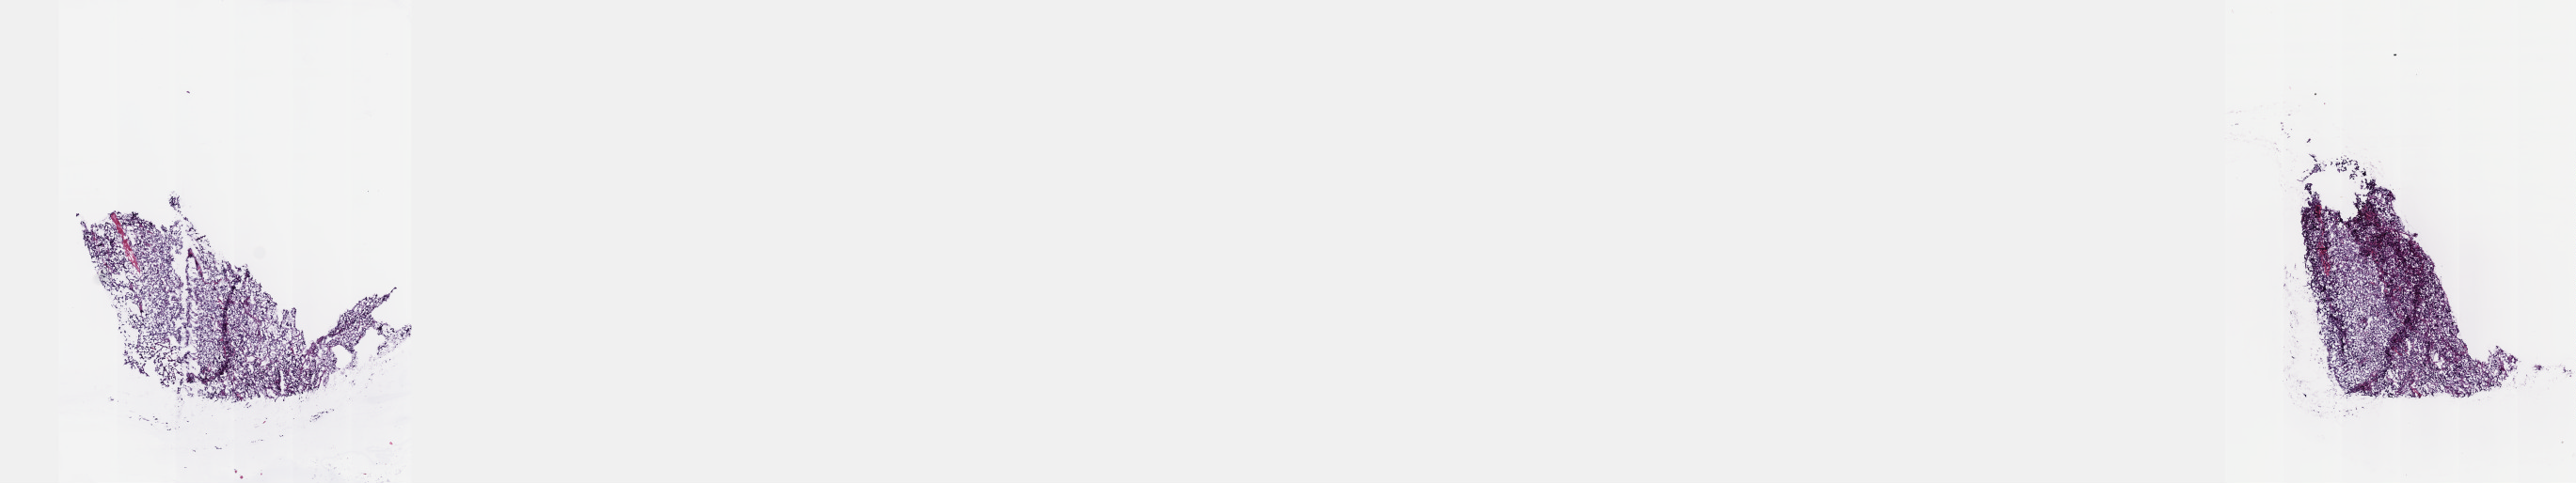
Whole-slide histology image, H&E — a low-resolution overview of the entire scanned area, about 22.1 x 4.2 mm (acquisition: 40x scan). Frozen section from the top of the tissue portion. Heart, mediastinum, and pleura, primary tumour sample. Female, age 47 years at initial diagnosis. Slide review estimates, as recorded: tumour cells 80%, tumour nuclei 80%, normal cells 0%, stromal cells 20%, necrosis 0%. Inflammatory infiltration, as recorded: lymphocyte infiltration 0%, monocyte infiltration 0%, neutrophil infiltration 0%.
Histologic diagnosis: Extra-adrenal paraganglioma, malignant (mediastinum, NOS).